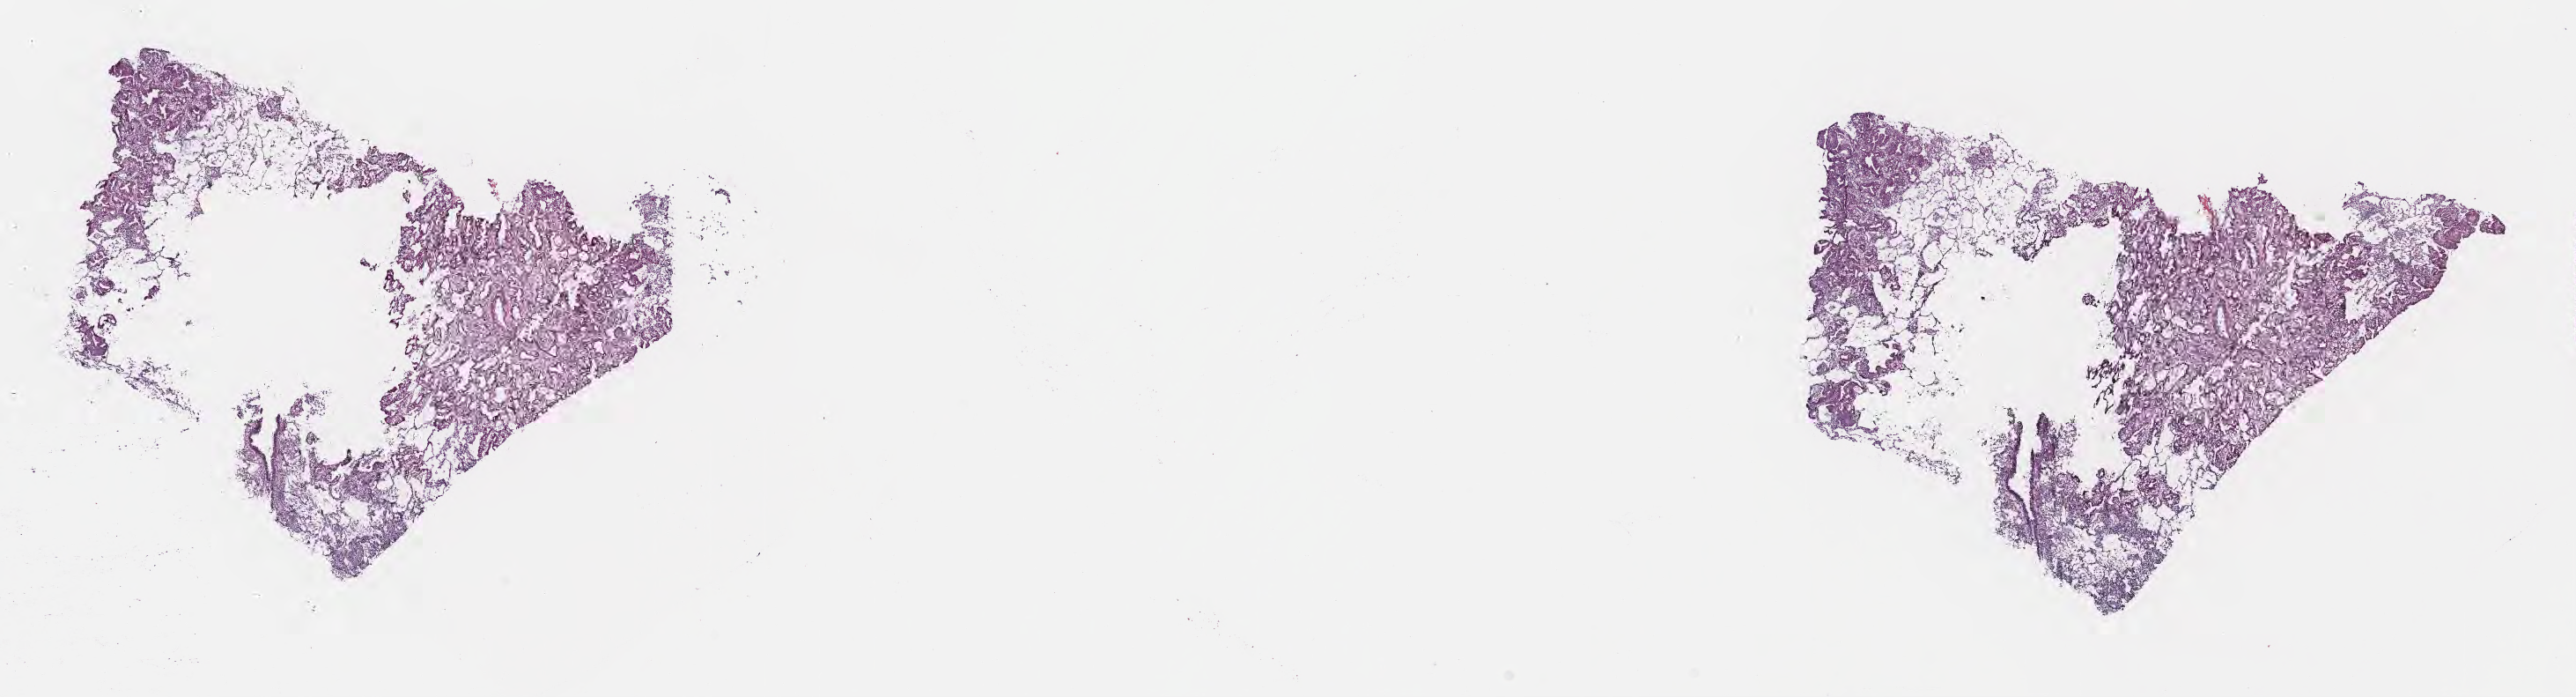
Whole-slide image, hematoxylin and eosin (H&E) stain — shown as a low-resolution overview of the whole scanned area (about 23.7 x 6.4 mm), cryosection, primary tumor, anatomic site: upper lobe of left lung. Female patient, 69 years old. Slide review estimates, as recorded: tumor cells 70%, tumor nuclei 70%, stromal cells 25%, necrosis 0%, normal cells 5%. Inflammatory infiltration, as recorded: lymphocyte infiltration 6%, monocyte infiltration 5%, neutrophil infiltration 6%.
Diagnosis: Adenocarcinoma with mixed subtypes. Section: top of the tissue portion. AJCC pathologic stage: Stage IB.